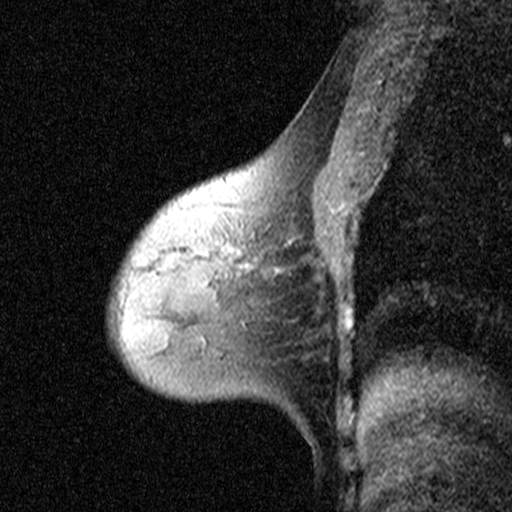
Breast MRI (dynamic contrast-enhanced), one sagittal slice; position 28 of 44 along the scan axis; dynamic contrast-enhanced study with each time point stored as its own series, time point 2 of 3 at this slice position (early post-contrast, ordered by acquisition time); 1.5 T; TE 4.5 ms, TR 11 ms; 3 mm slice thickness; 512 × 512 image matrix, field of view 200 × 200 mm. Female patient, age 53 years. From the clinical record (not read from this slice): setting: breast cancer imaged before/during neoadjuvant chemotherapy; receptor status: HR-positive, HER2-negative.
Structures marked on this image (semi-automatically segmented with operator editing):
- analysis volume of interest (the breast-tissue region the enhancement analysis was run in; not a lesion): bounding box <186,216,307,311> (left, top, right, bottom; pixels)
- tumour enhancement mask (voxels above the 90 % enhancement threshold inside the analysis volume of interest): <225,244,247,268>